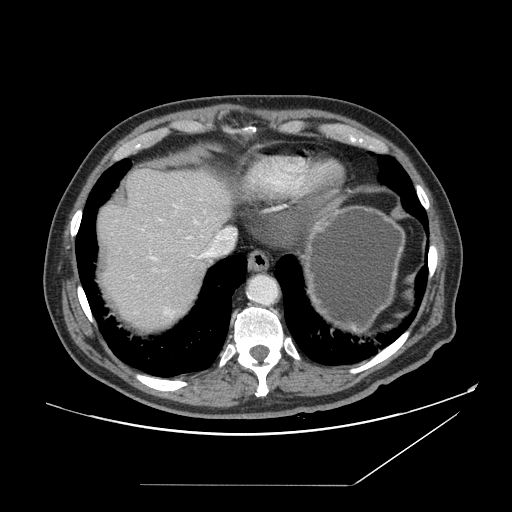
Contrast-enhanced abdominal CT, one axial slice; position 133 of 166 along the scan axis; 120 kVp; intravenous contrast given; soft-tissue window (W 400 / L 40 HU); 2.5 mm slice thickness; 512 × 512 image matrix, field of view 416 × 416 mm. Male patient, age 80 years. Case-level facts recorded for this patient, not image findings: diagnosis: colorectal cancer liver metastases, imaged before liver resection; multiple liver metastases: no; largest metastasis: 2.2 cm; chemotherapy before resection: no.
Annotated regions visible in this slice (expert manual segmentation):
- hepatic veins: bounding box [x1, y1, x2, y2] px = [149, 219, 236, 260]
- liver: [97, 168, 235, 332]
- planned liver remnant (the part of the liver to remain after resection): [97, 168, 235, 259]
- portal vein (with intrahepatic branches): [176, 206, 178, 208]